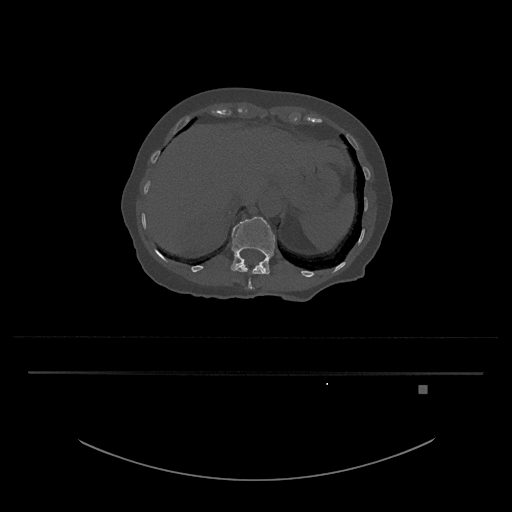
CT including the spine, one axial slice; position 579 of 797 along the scan axis; reconstruction kernel Br40s/3; 120 kVp; bone window (W 1800 / L 400 HU); 0.5 mm slice thickness; 512 × 512 image matrix, field of view 500 × 500 mm. Patient: female, 57 years. Case-level facts recorded for this patient, not image findings: primary cancer: cervical.
Structures marked on this image (semi-automatically segmented with operator editing):
- L1 vertebra: bounding box [x1, y1, x2, y2] px = [231, 217, 275, 275]
- T12 vertebra: [235, 263, 265, 289]